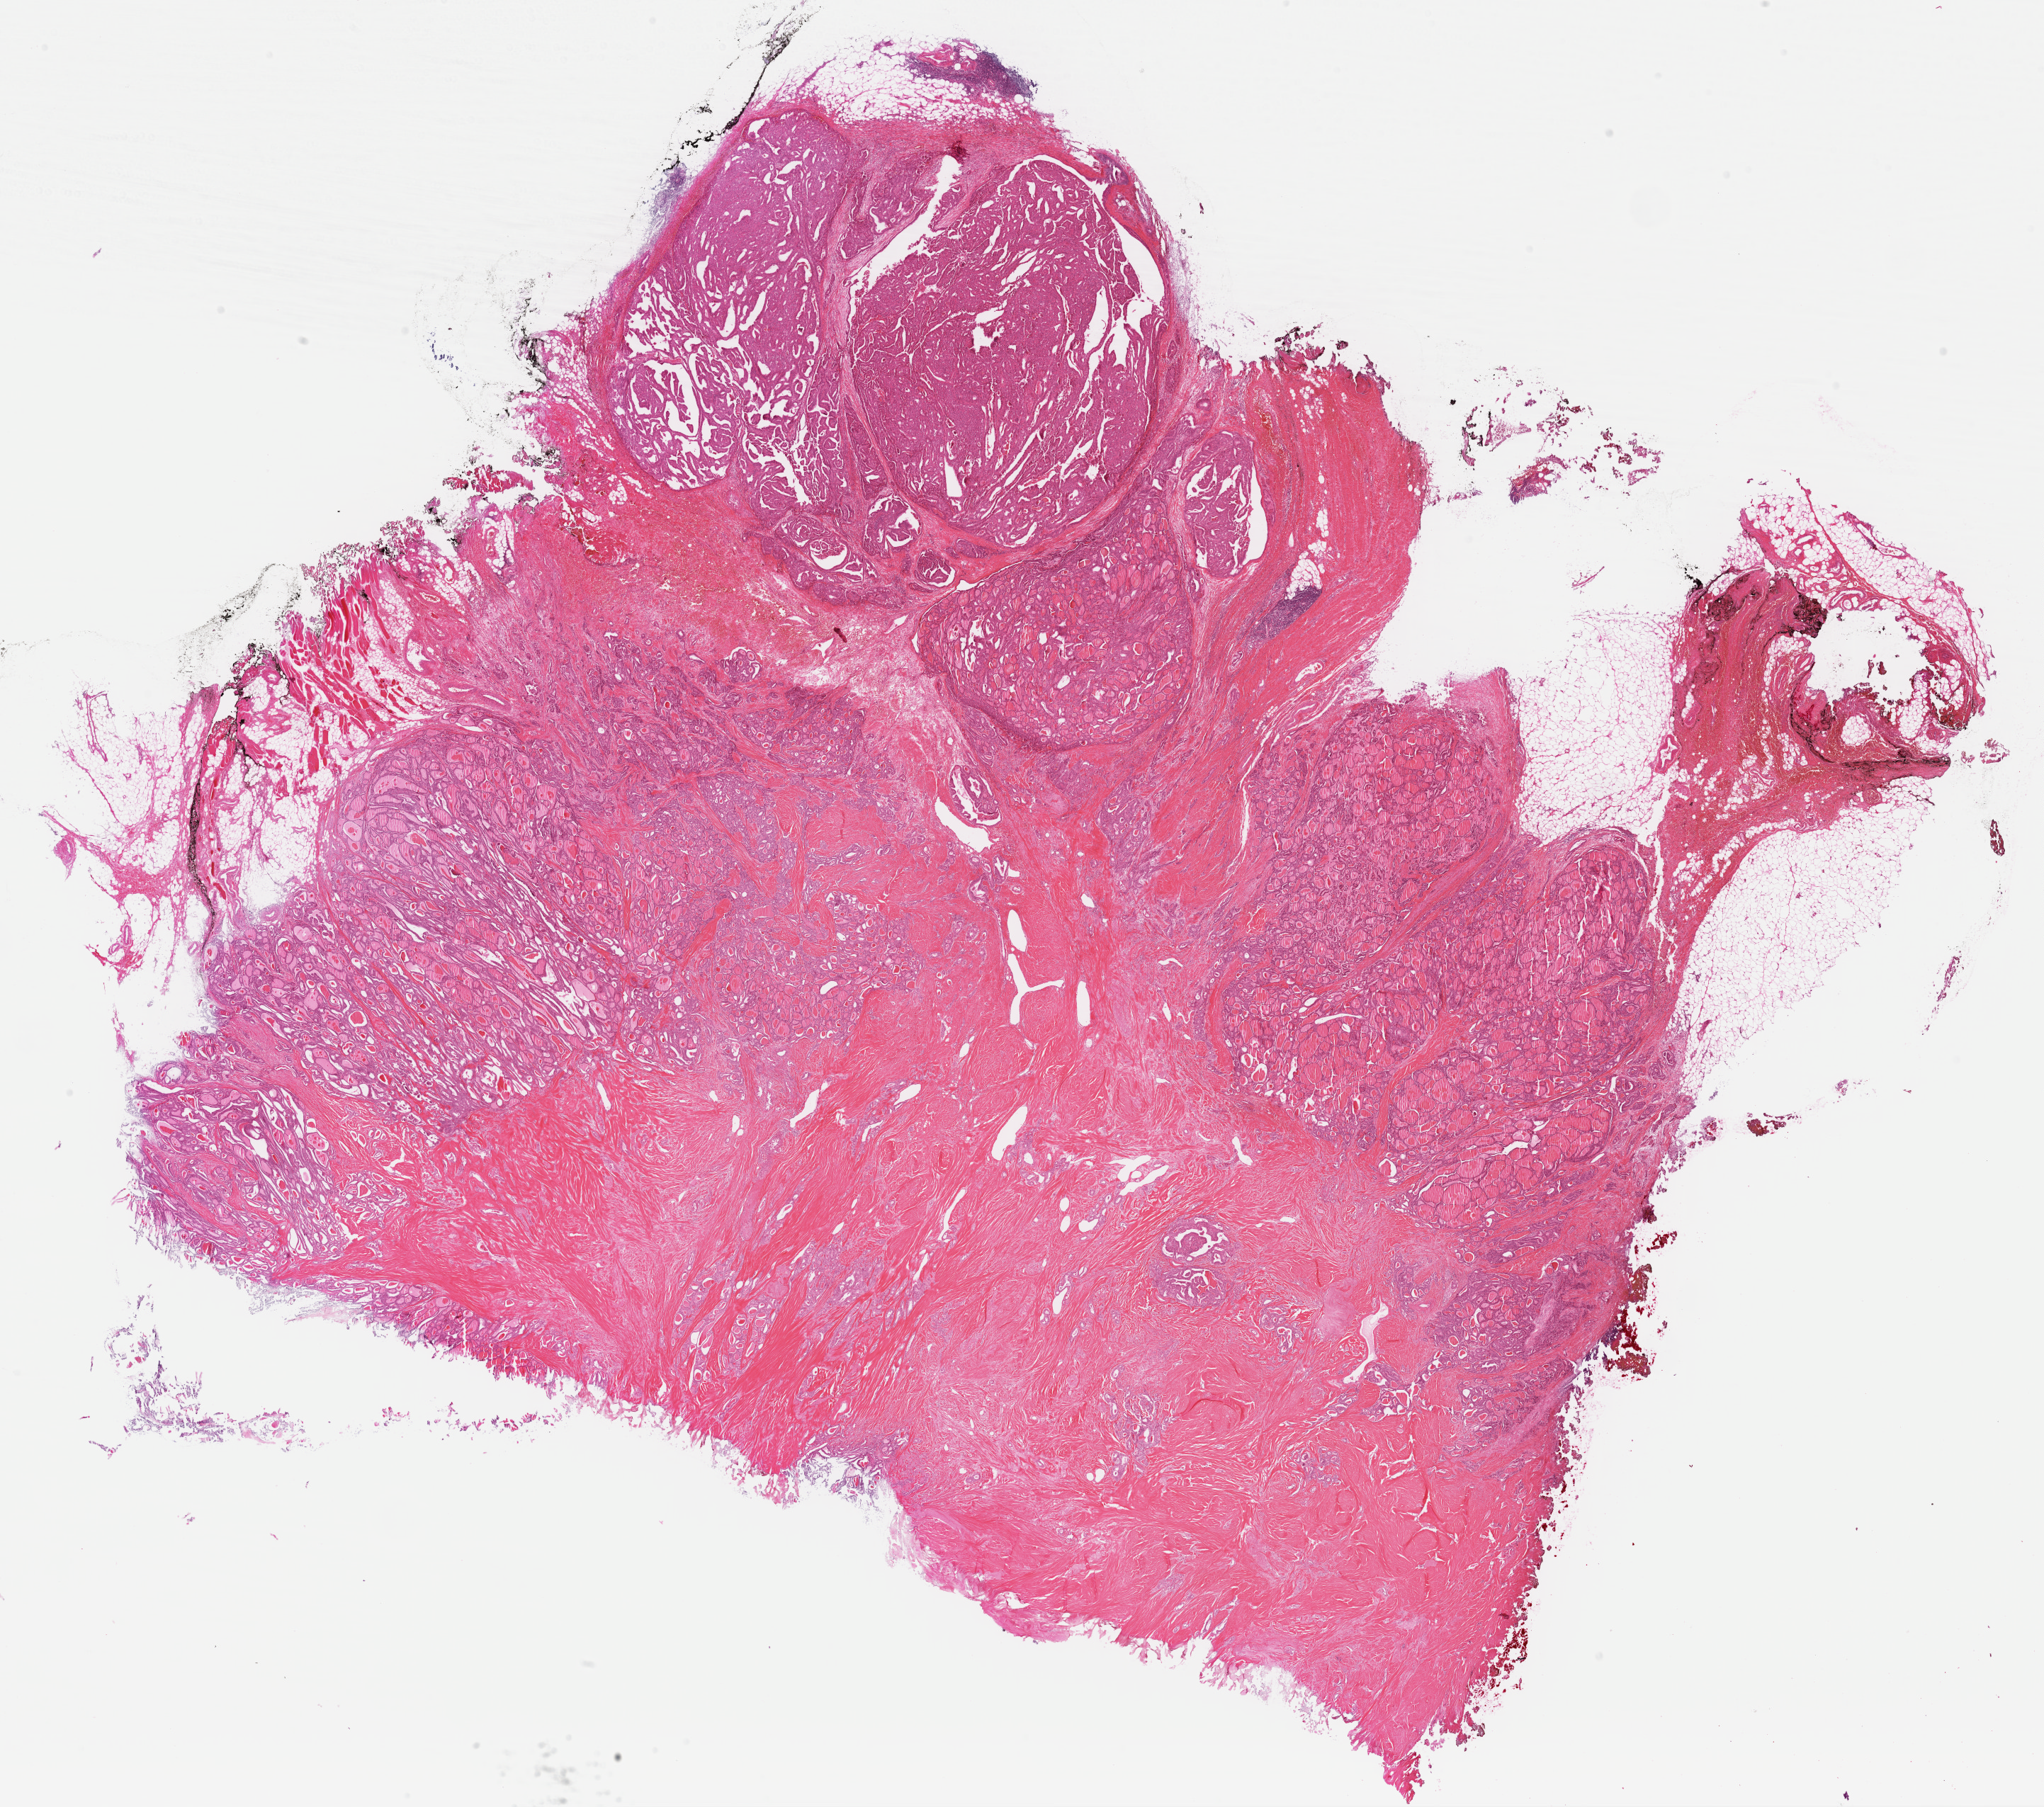
Whole-slide histology image, H&E, whole scanned area (about 22.8 x 20.2 mm, slide scanned at 40x) shown as a low-resolution overview, FFPE section, primary tumour sample from the thyroid. Female, age 64 years at initial diagnosis.
AJCC pathologic stage: III. Diagnosis: Papillary adenocarcinoma, NOS (thyroid gland).